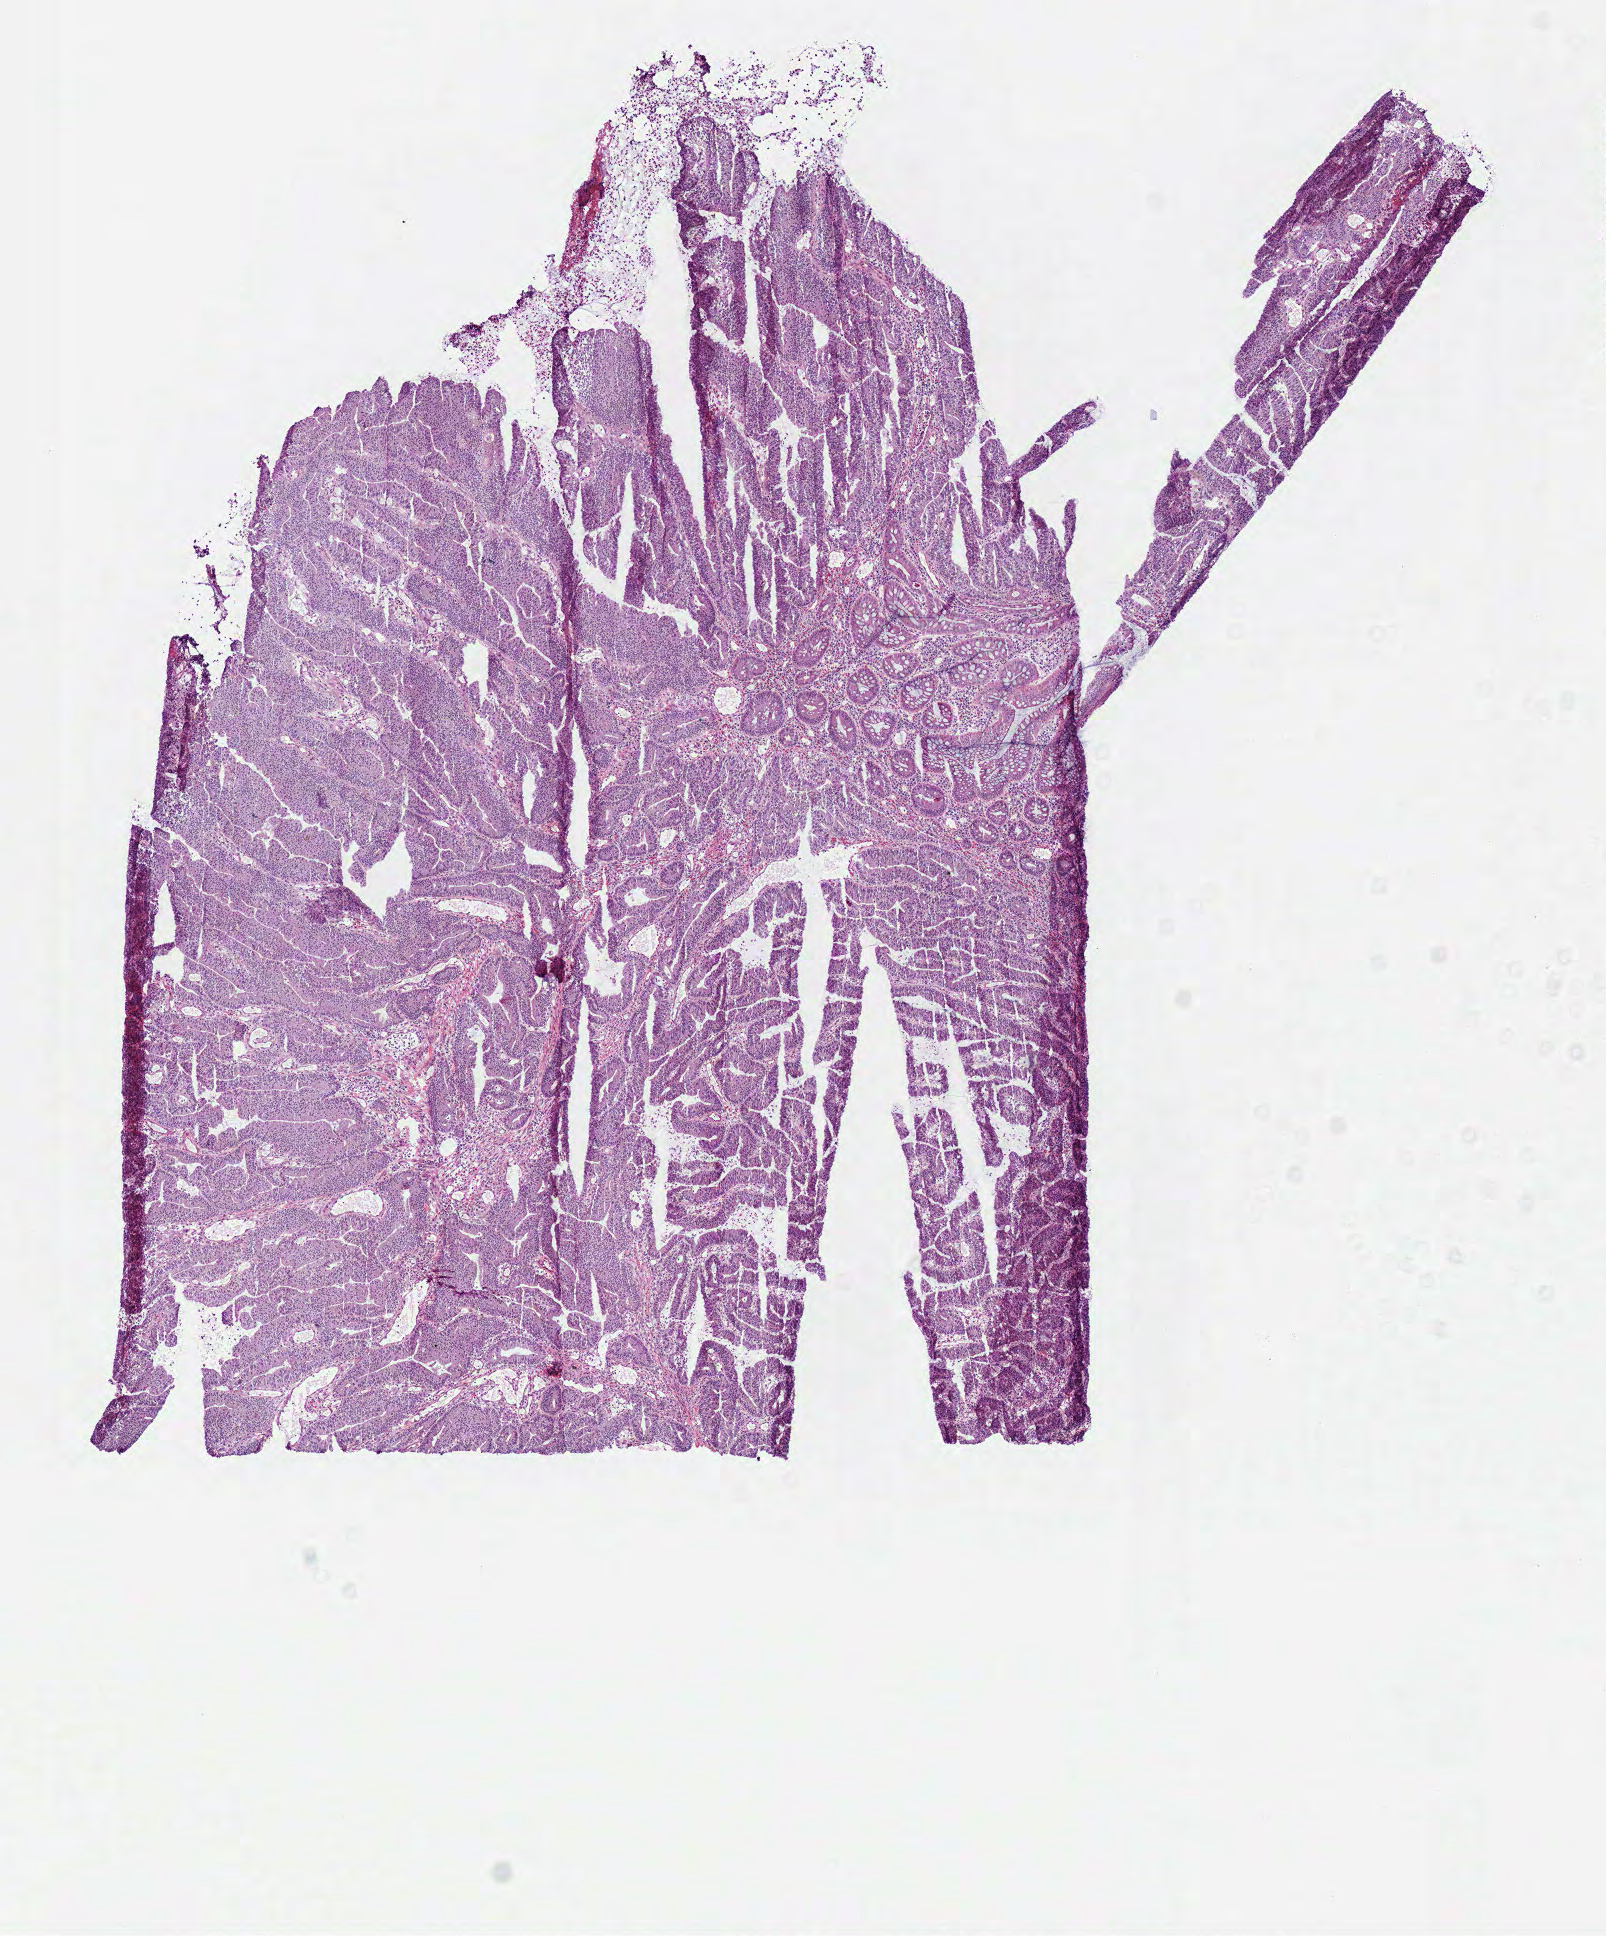
Whole-slide histology image, H&E-stained — shown as a low-resolution overview of the whole scanned area (about 6.3 x 7.6 mm, acquisition: 40x scan). Frozen section from the bottom of the tissue portion. Primary tumour sample from the rectum. Patient: male, age at initial diagnosis 59 years. Slide review estimates, as recorded: tumour cells 87%, tumour nuclei 85%.
Pathologic diagnosis: Adenocarcinoma with mixed subtypes.